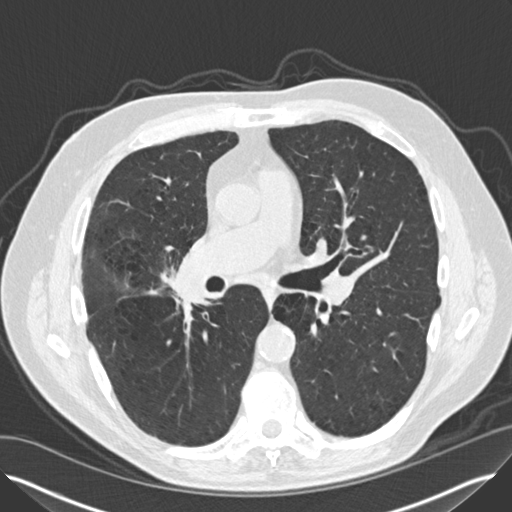
Low-dose screening chest CT, one axial slice; position 79 of 149 along the scan axis; lung window (W 1500 / L -600 HU); 2 mm slice thickness; 512 × 512 image matrix, field of view 370 × 370 mm.
Outlined on this slice (manually delineated by an expert):
- lesion 2 (tumor, hilum of right lung): box from (x=179, y=275) to (x=207, y=303) px